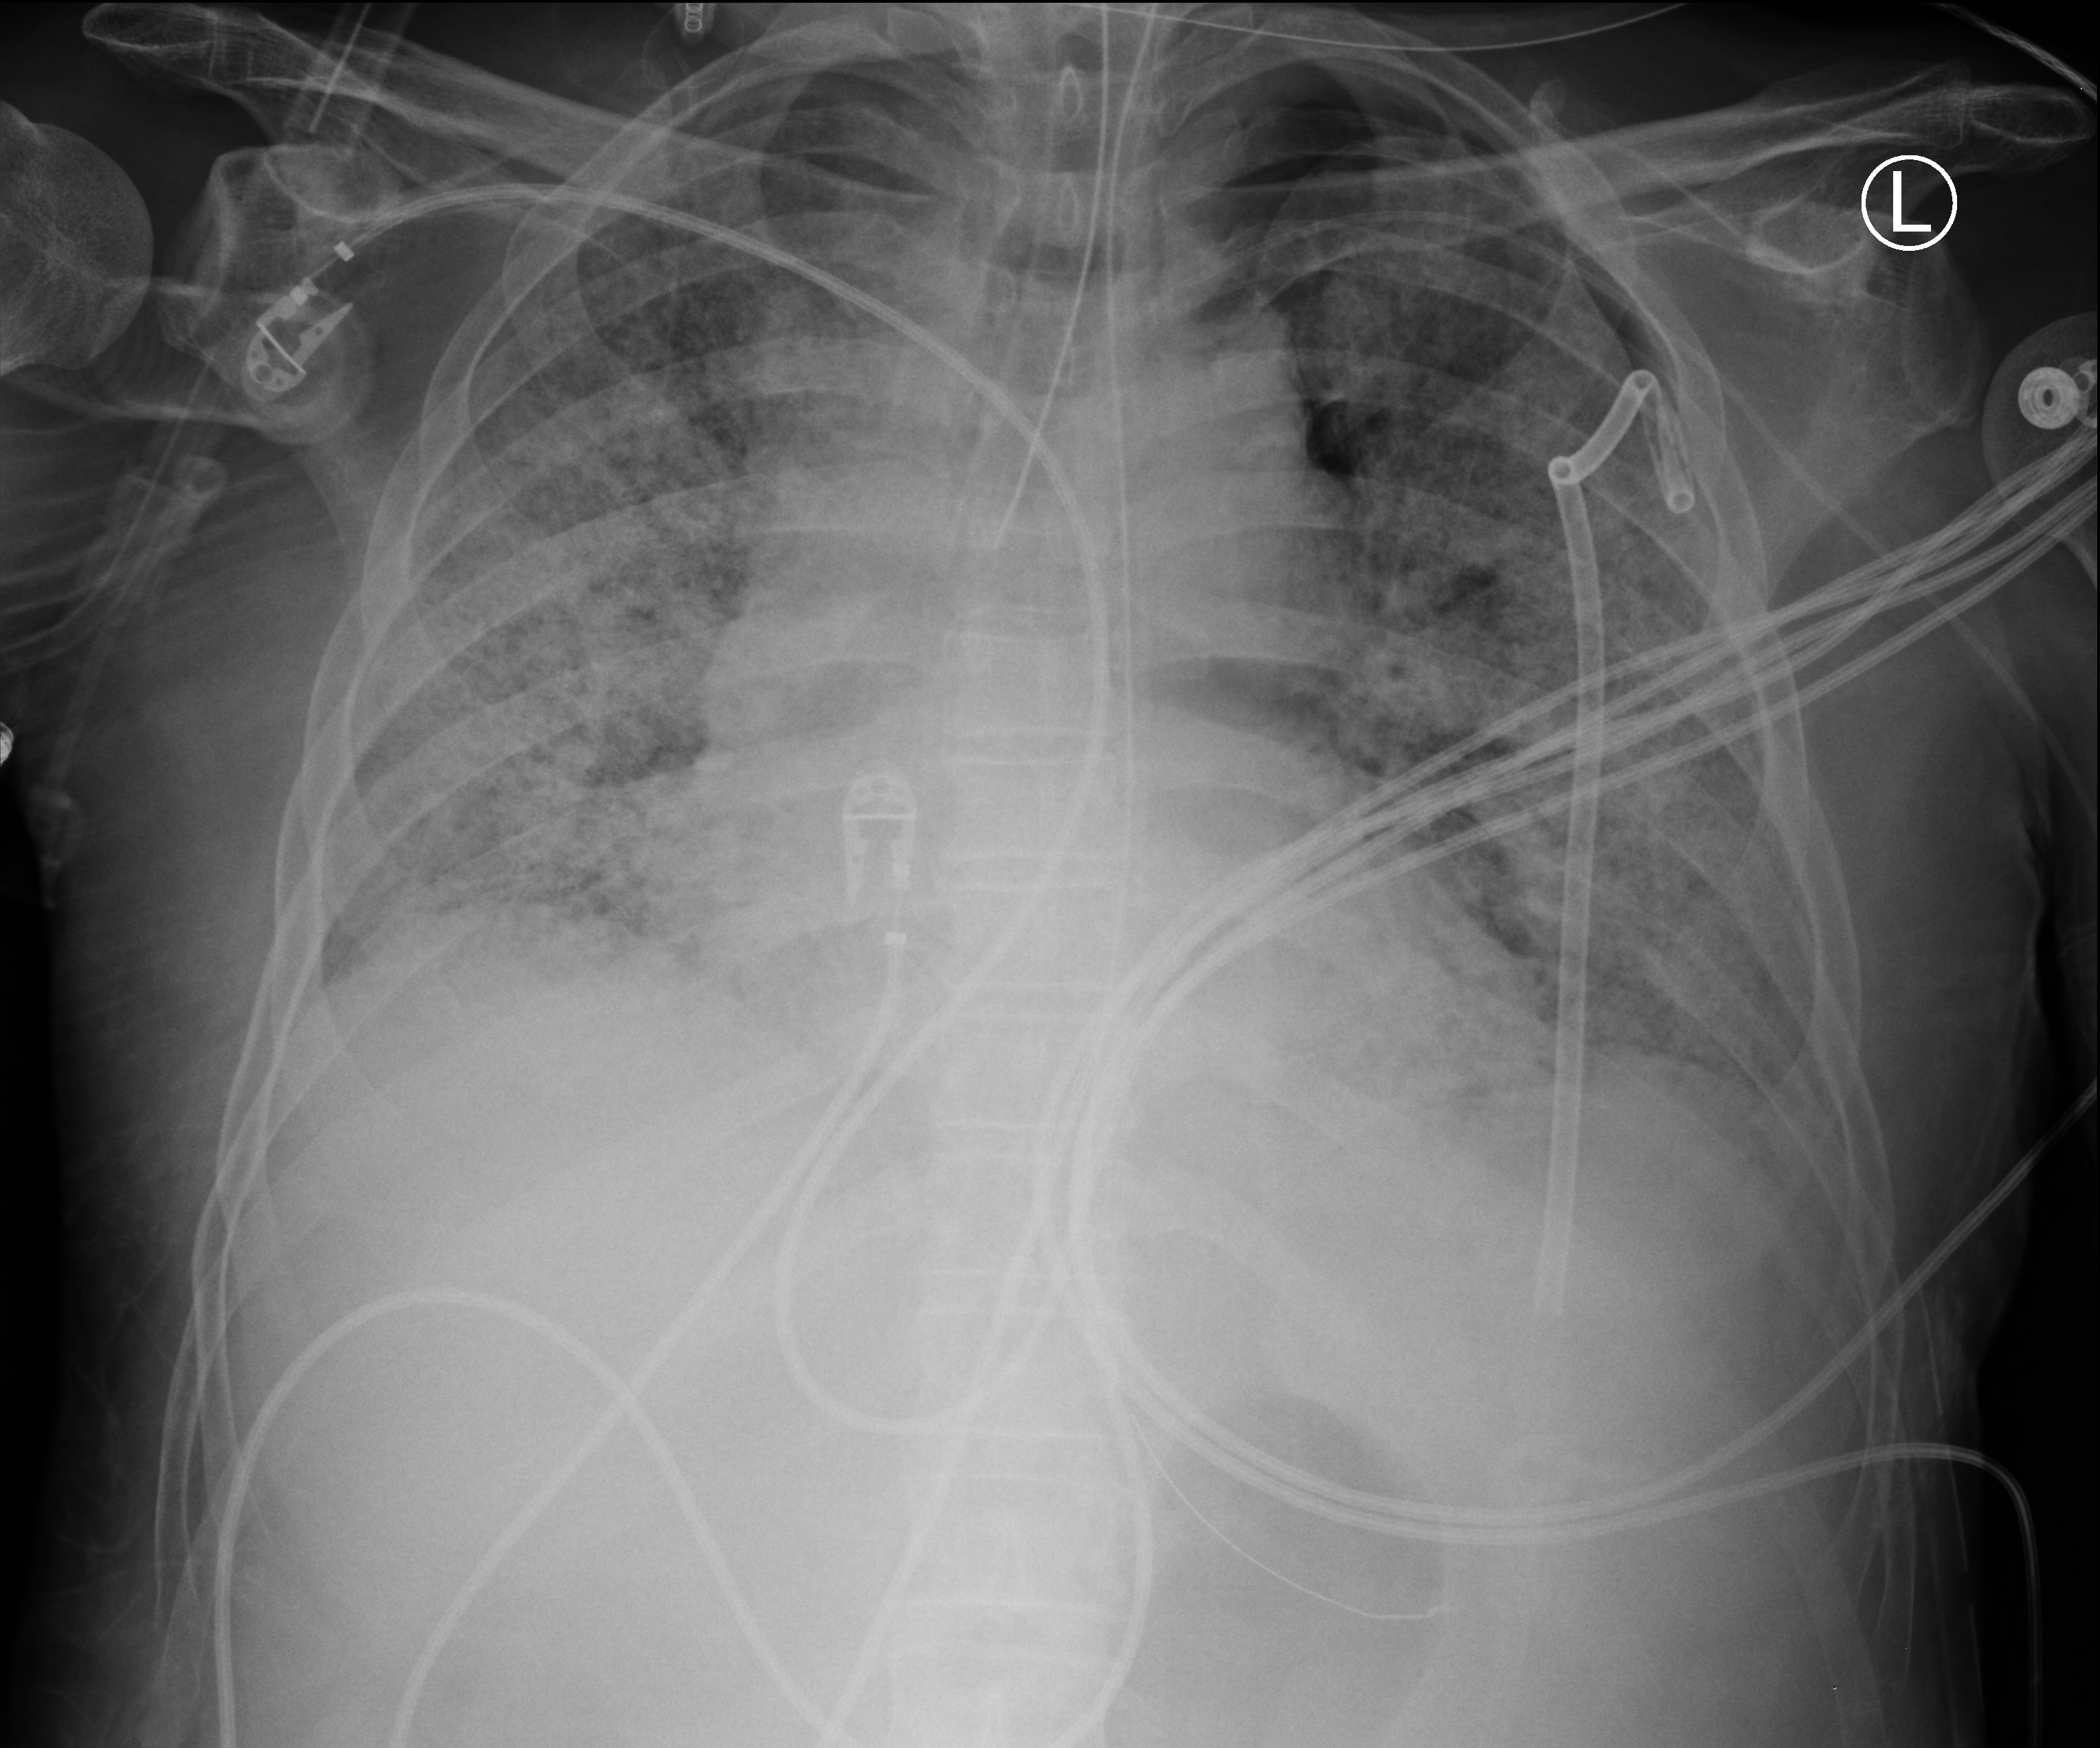
Chest X-ray (portable); anteroposterior (AP) projection. Male patient hospitalised with COVID-19, age 60–74 years.
Admission-level facts for this patient (not findings on this image; timing relative to this image not recorded):
- admitted to intensive care during this hospital stay: yes